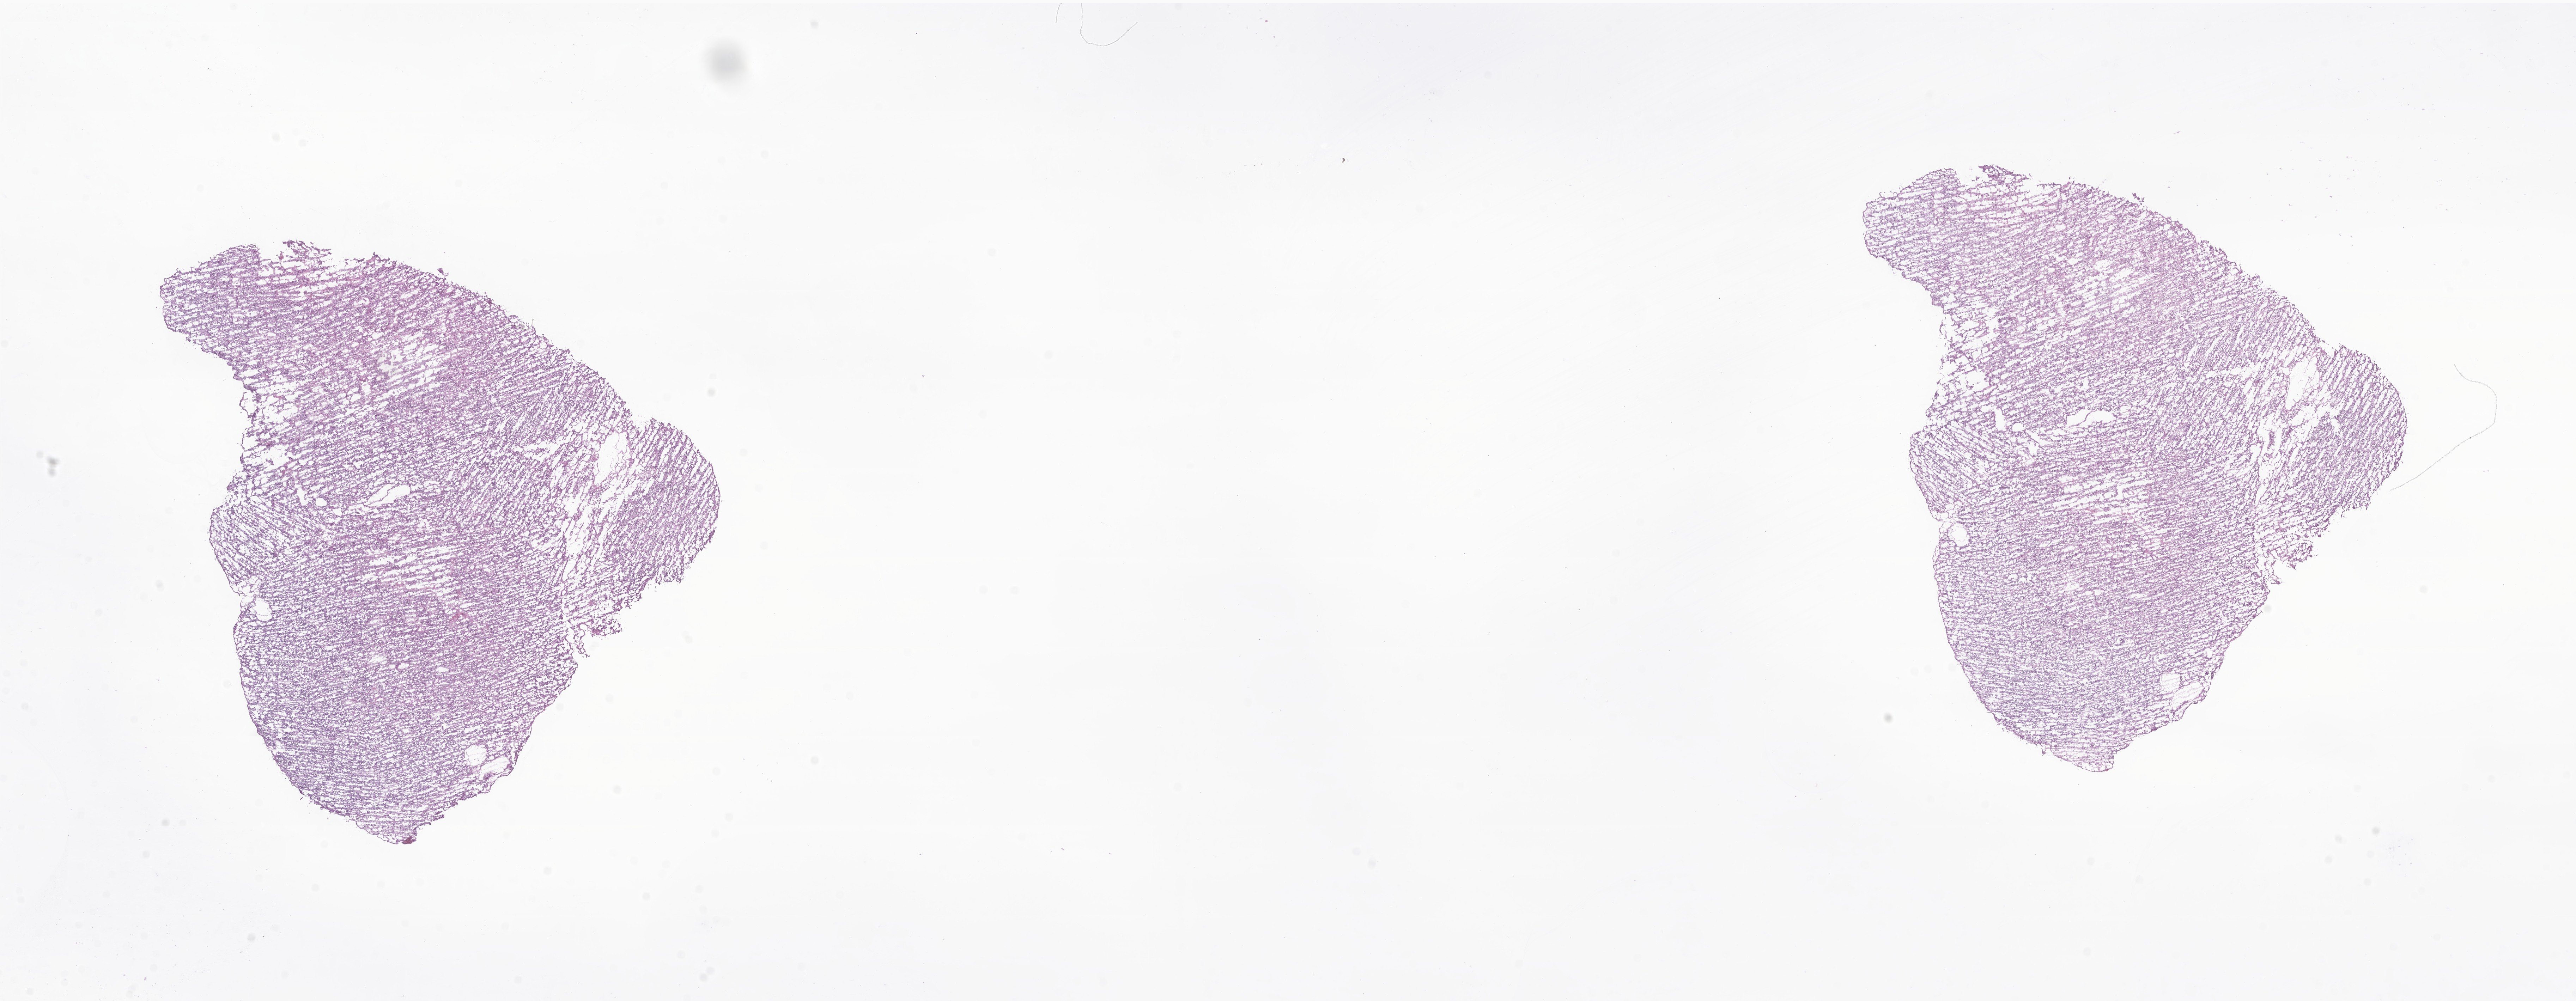
H&E whole-slide image of tumor tissue from the brain — a low-resolution overview of the entire scanned area, about 30.8 x 12.0 mm; frozen section (OCT-embedded). Patient: male, age 994 days.
Diagnosis: Ependymoma, NOS.